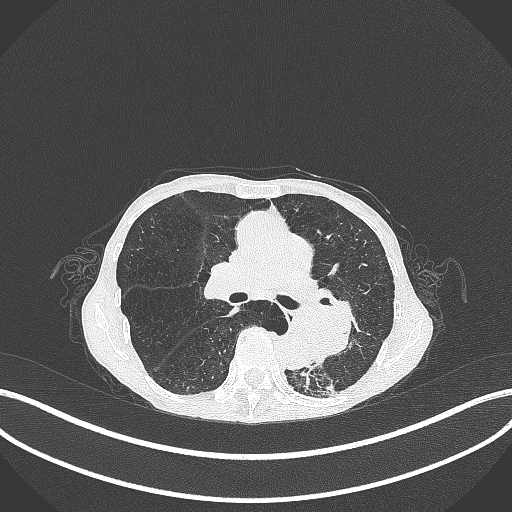
Chest CT, one axial slice. Slice 163 of 347 in the series (ordered by position). Reconstruction kernel B70f. Lung window (W 1500 / L -600 HU). 1 mm slice thickness. 512 × 512 image matrix, field of view 400 × 400 mm. Patient: female, 70 years. From the clinical record (not read from this slice): clinical TNM (as recorded): T3 N0 M0; histopathological grade: G3.
Structures marked on this image (bounding box drawn by a radiologist):
- lung tumour (recorded histology: small cell carcinoma): bounding box (x1, y1, x2, y2) in pixels: (287, 301, 357, 364)